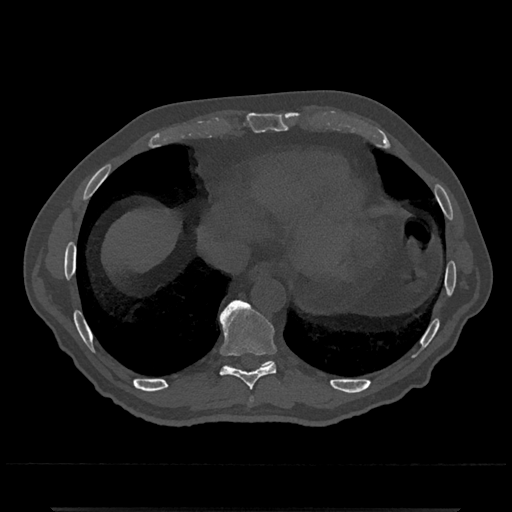
CT including the spine, one axial slice. Position 602 of 797 along the scan axis. Bone window (W 1800 / L 400 HU). 512 × 512 image matrix, field of view 393 × 393 mm. Patient: male, 67 years. From the clinical record (not read from this slice): primary cancer: prostate.
Outlined on this slice (semi-automatically segmented with operator editing):
- T10 vertebra: box from (x=262, y=361) to (x=274, y=366) px
- T8 vertebra: (x=251, y=398)–(x=253, y=401)
- T9 vertebra: (x=219, y=299)–(x=276, y=390)